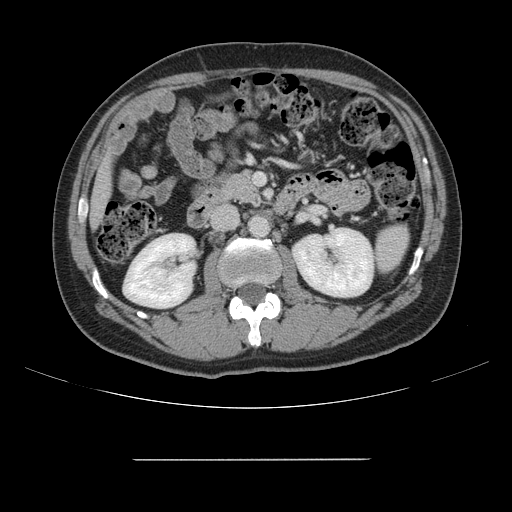
Contrast-enhanced abdominal CT, one axial slice. Slice 56 of 164 in the series (ordered by position). Intravenous contrast given. Soft-tissue window (W 400 / L 40 HU). 512 × 512 image matrix, field of view 404 × 404 mm. Male patient, age 54 years. From the clinical record (not read from this slice): diagnosis: colorectal cancer liver metastases, imaged before liver resection; multiple liver metastases: yes; largest metastasis: 1 cm; chemotherapy before resection: yes.
Structures marked on this image (manually delineated by an expert):
- liver: bounding box <92,164,110,220> (left, top, right, bottom; pixels)
- planned liver remnant (the part of the liver to remain after resection): <92,165,109,222>